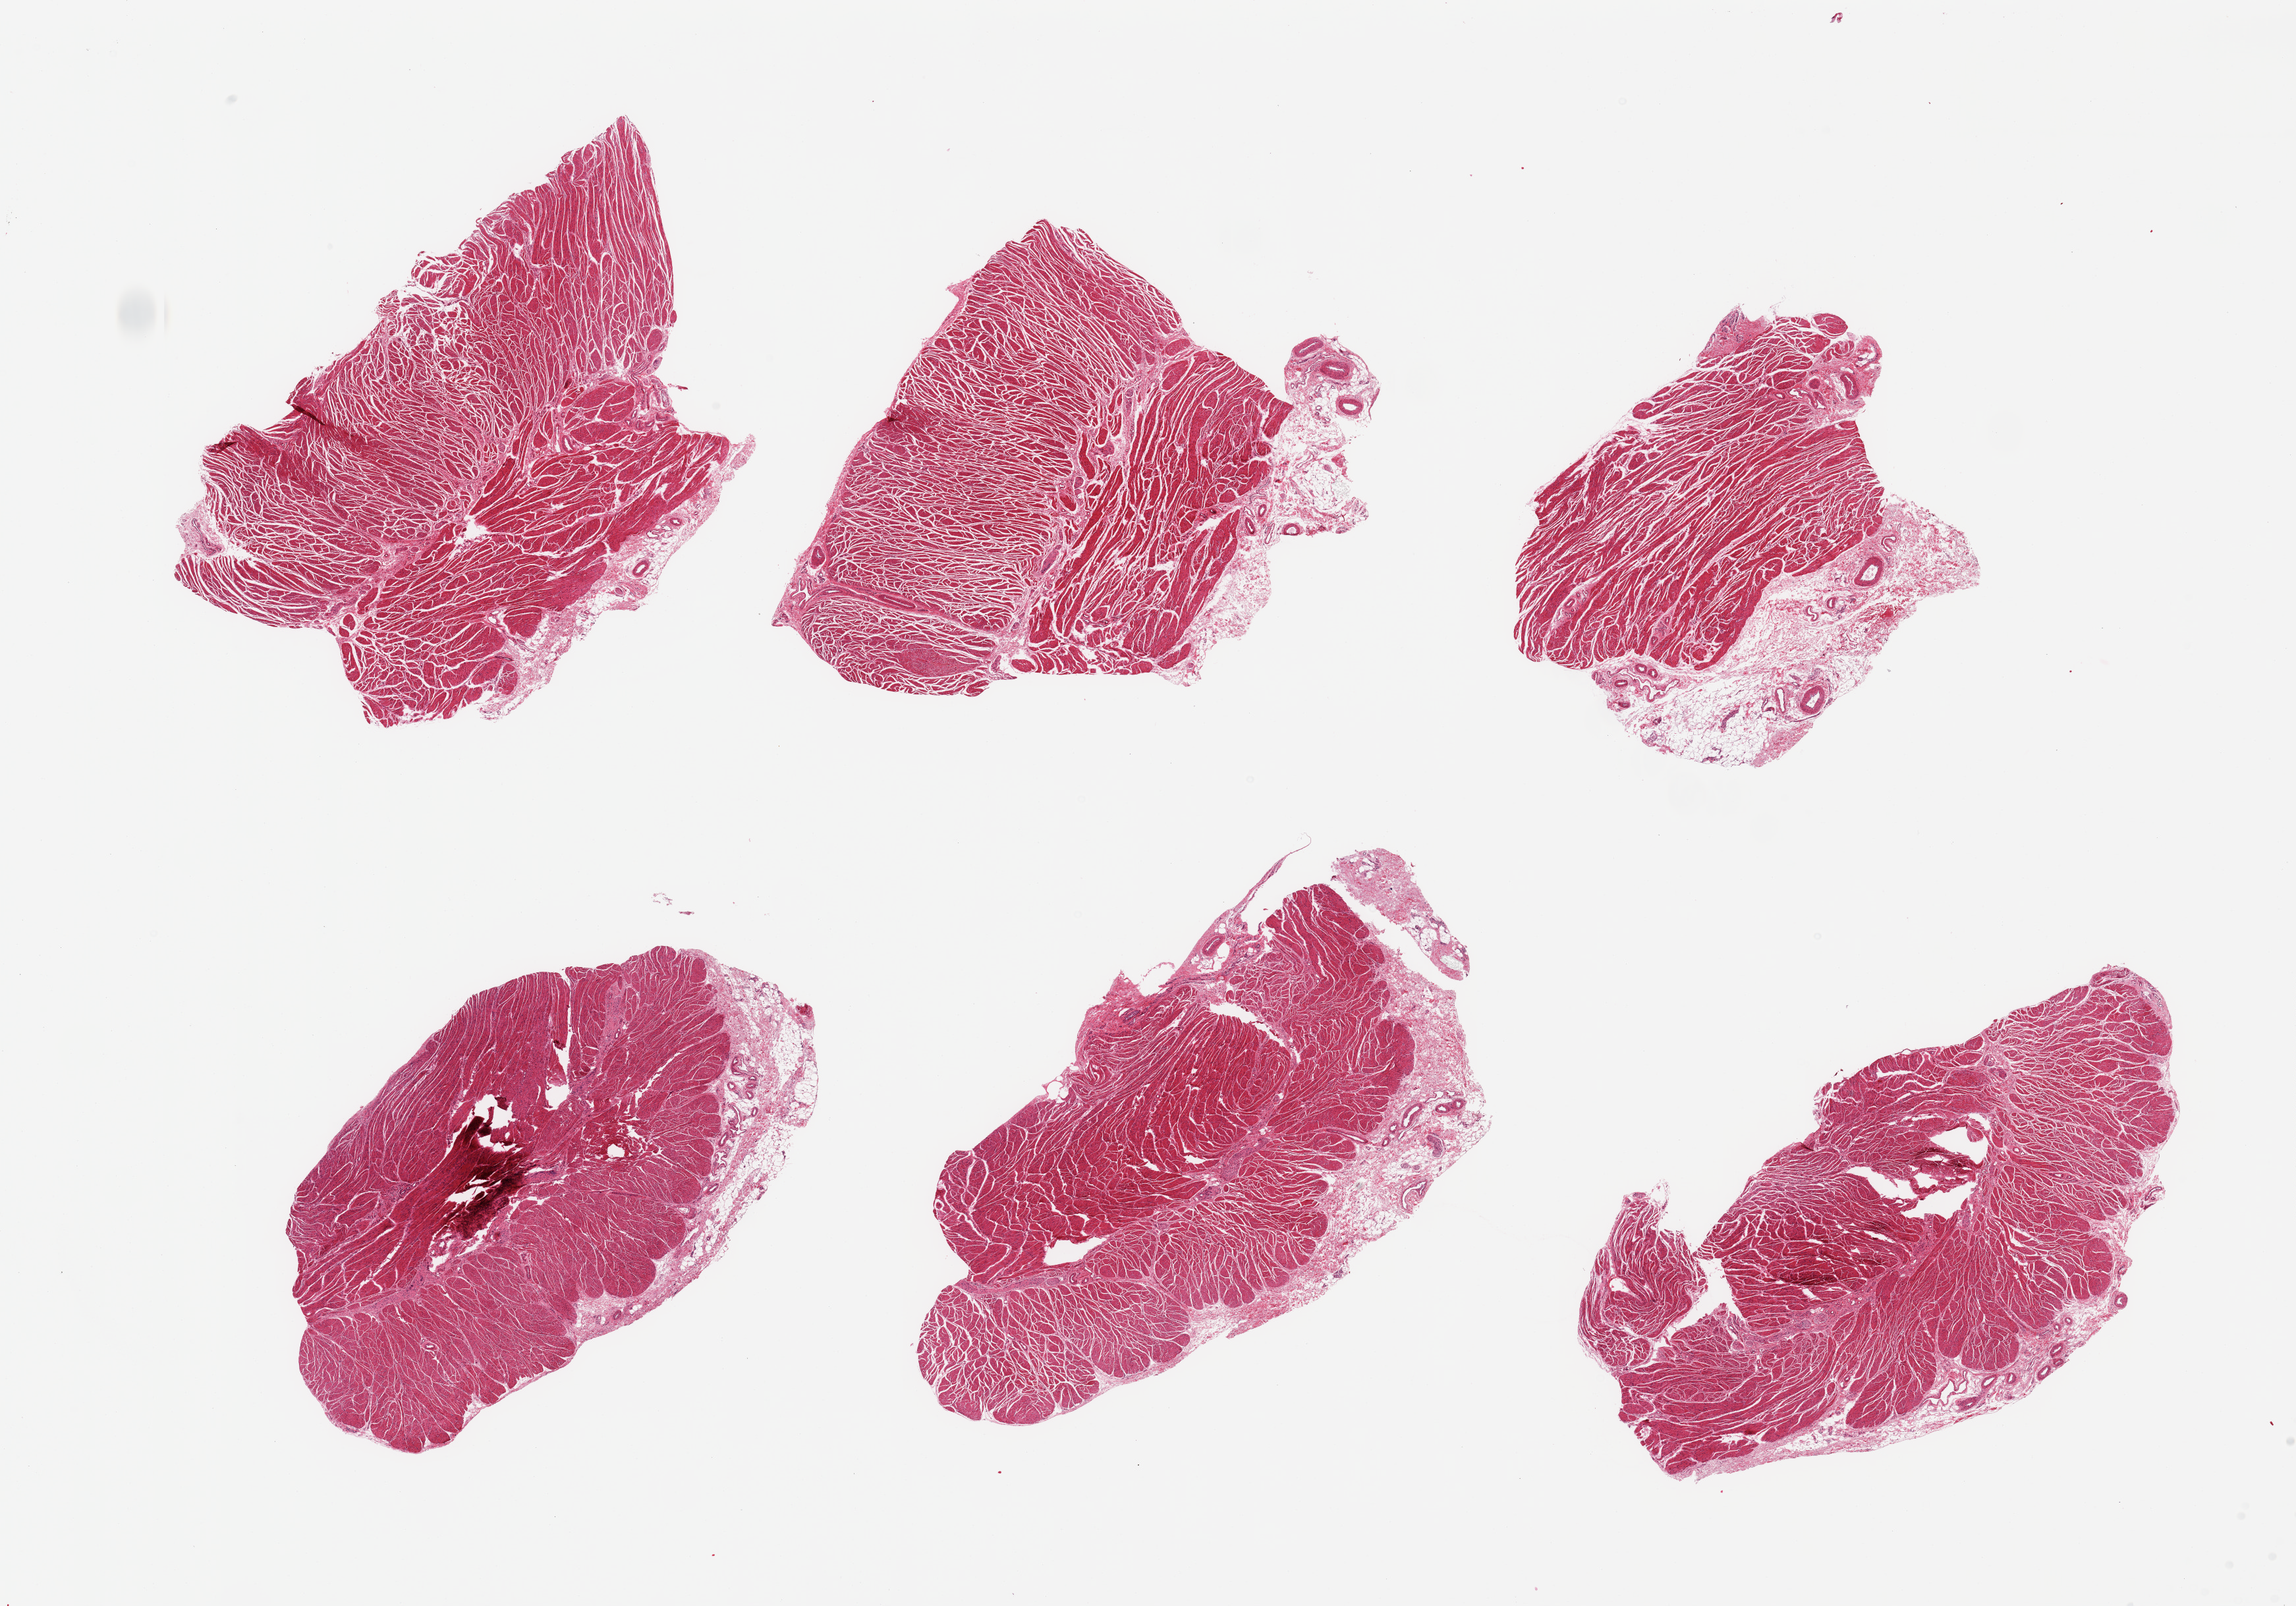
Haematoxylin and eosin whole-slide image, brightfield, a low-resolution overview of the entire scanned area, about 27.6 x 19.3 mm, PAXgene-fixed, paraffin-embedded tissue, sampled site (target tissue): gastroesophageal junction, donor tissue sample. Male donor.
Reviewer comment on this tissue sample: 6 pieces; target muscularis and up to 1.6mm loose connective tissue.